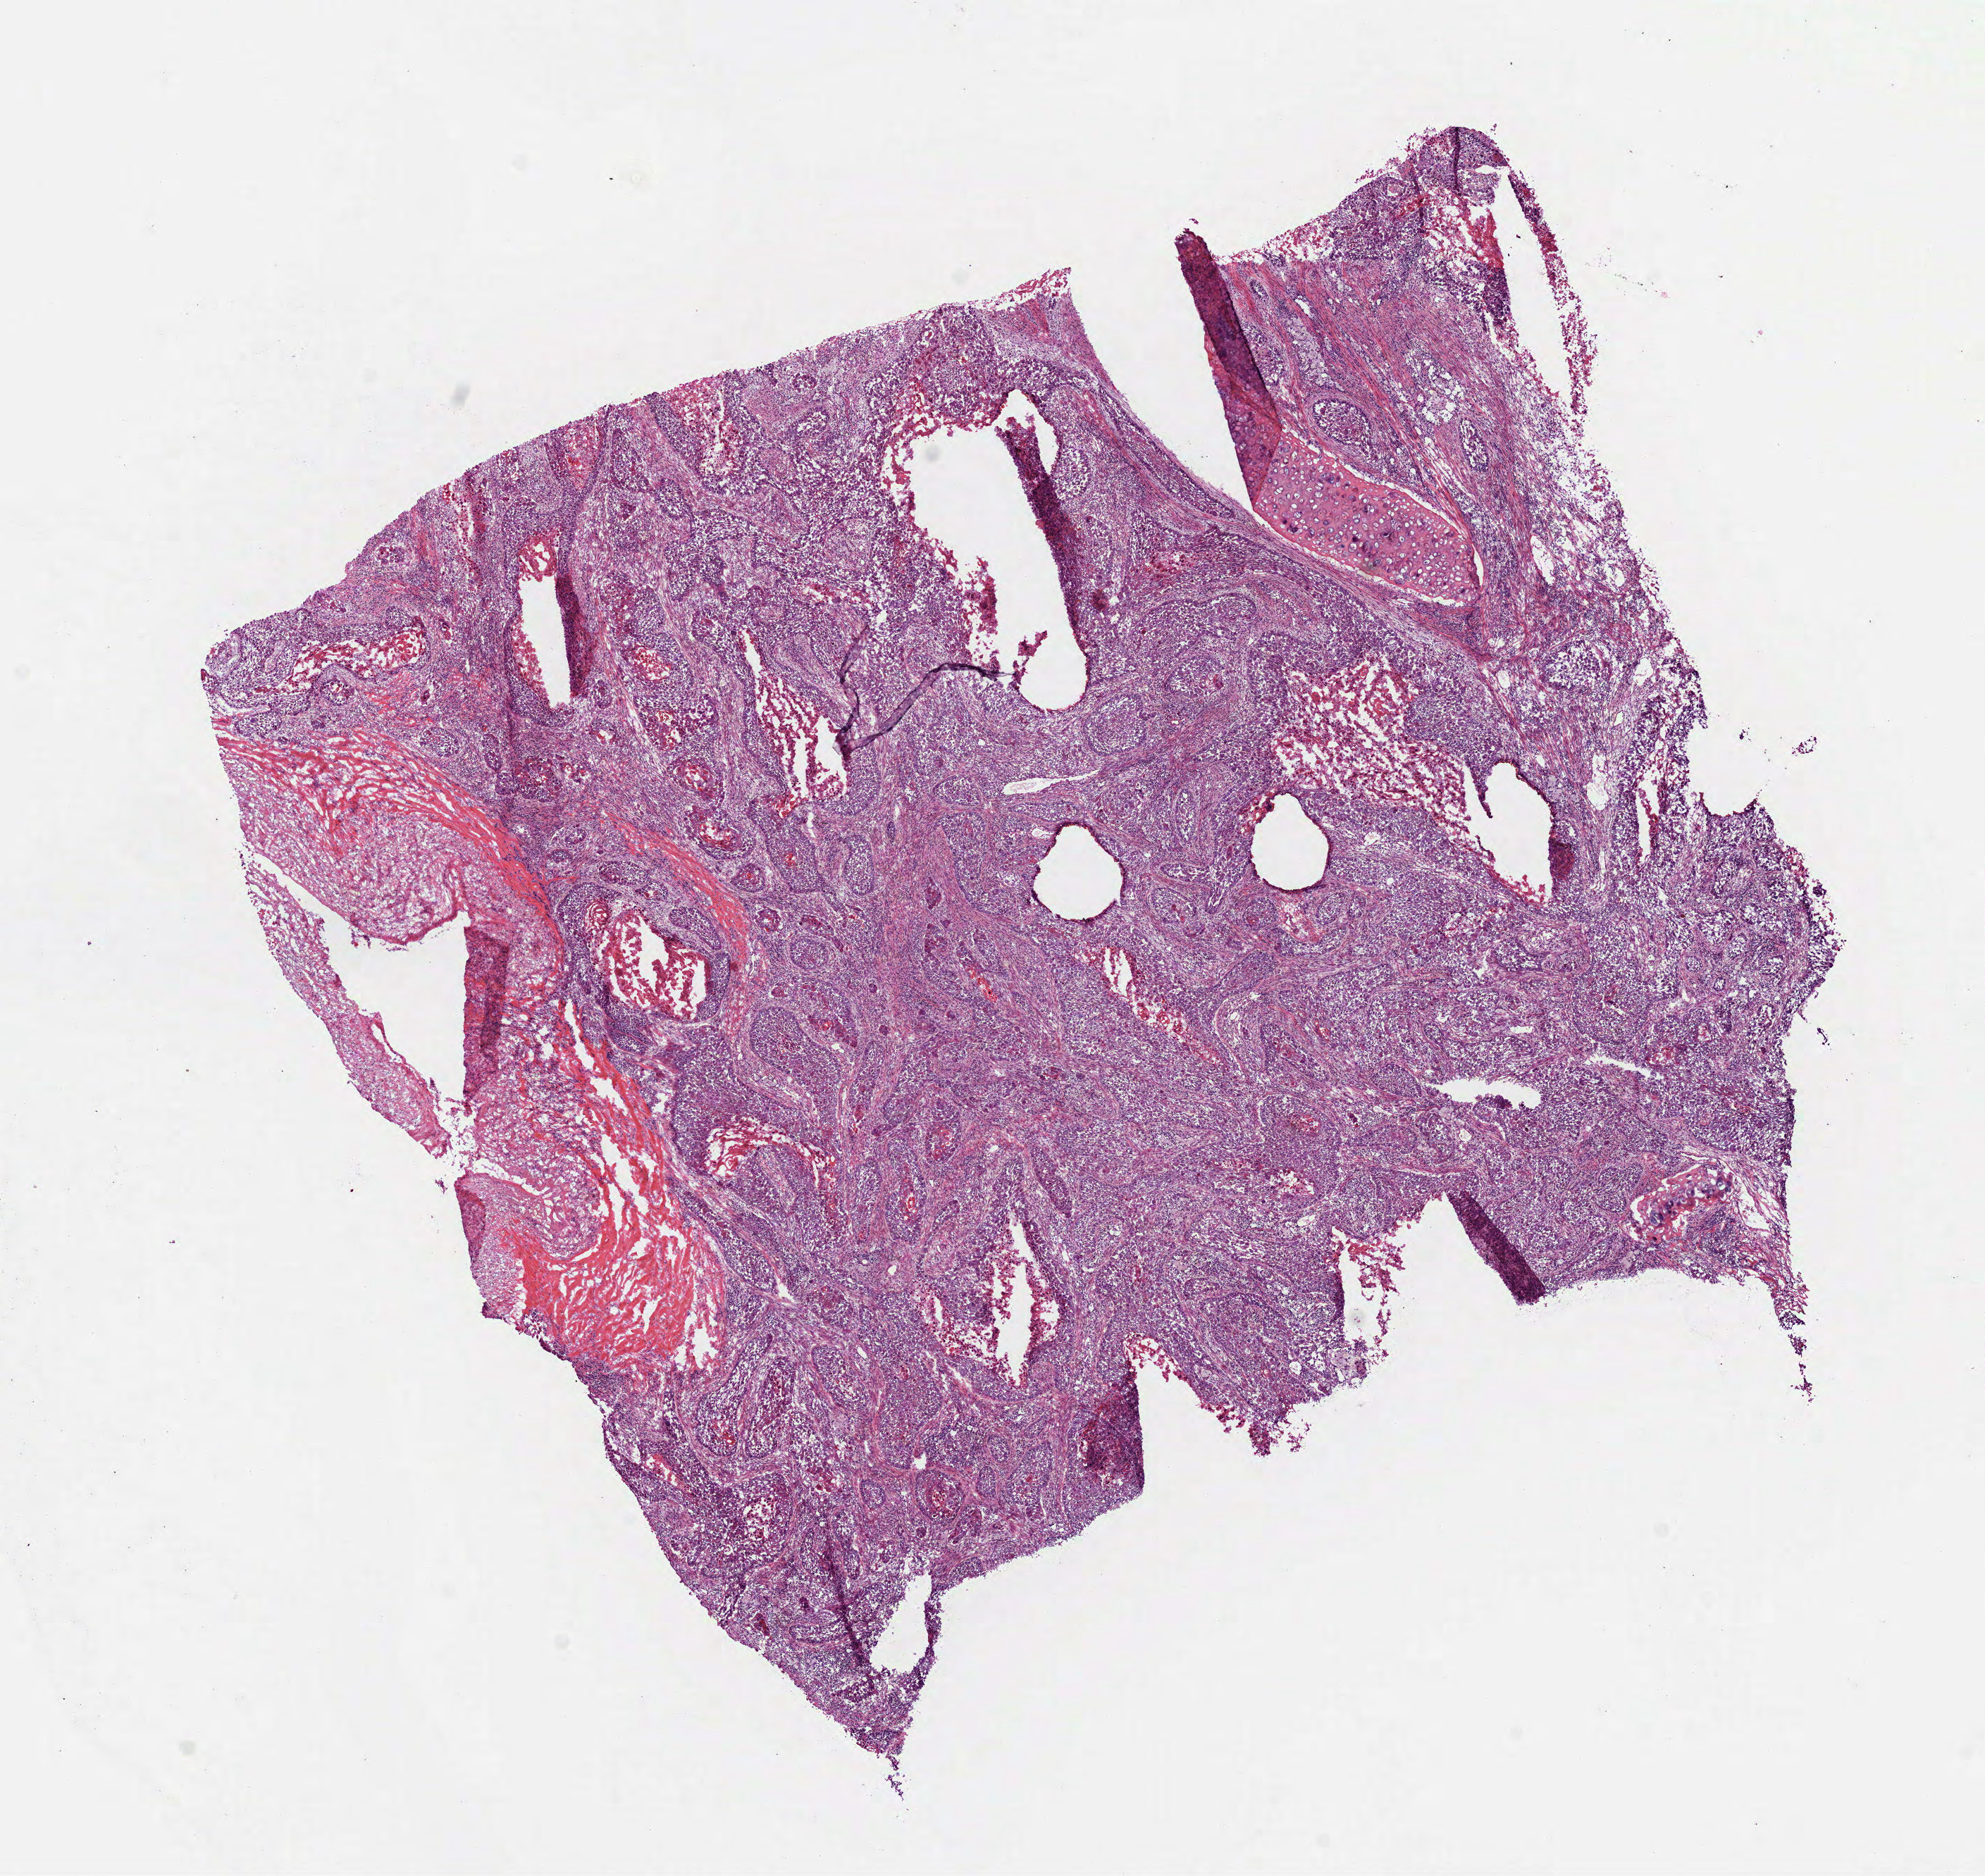
Whole-slide histology image, H&E — whole scanned area (about 11.4 x 10.7 mm) shown as a low-resolution overview. Frozen section. Lung, primary tumour sample. Male, age 71 years at initial diagnosis. Pathologist review of this section (percent, as recorded): tumour cells 85%, tumour nuclei 65%, normal cells 0%, stromal cells 10%, necrosis 5%.
AJCC pathologic stage: IB (7th edition). Pathologic diagnosis: Squamous cell carcinoma, NOS (upper lobe, lung).